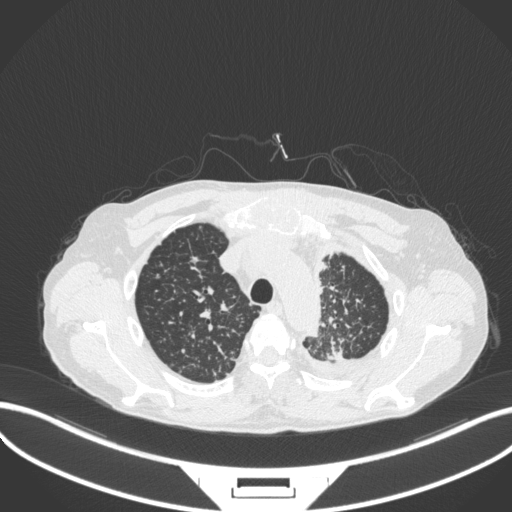
Chest CT, one axial slice; position 281 of 319 along the scan axis; reconstruction kernel B31f; 120 kVp; lung window (W 1500 / L -600 HU); 1 mm slice thickness; 512 × 512 image matrix, field of view 400 × 400 mm. Patient: male, 58 years. Case-level facts recorded for this patient, not image findings: clinical TNM (as recorded): T1c N3 M1.
Annotated regions visible in this slice (rectangle marked by the reading radiologist):
- lung tumour (recorded histology: adenocarcinoma): box from (x=327, y=337) to (x=344, y=362) px